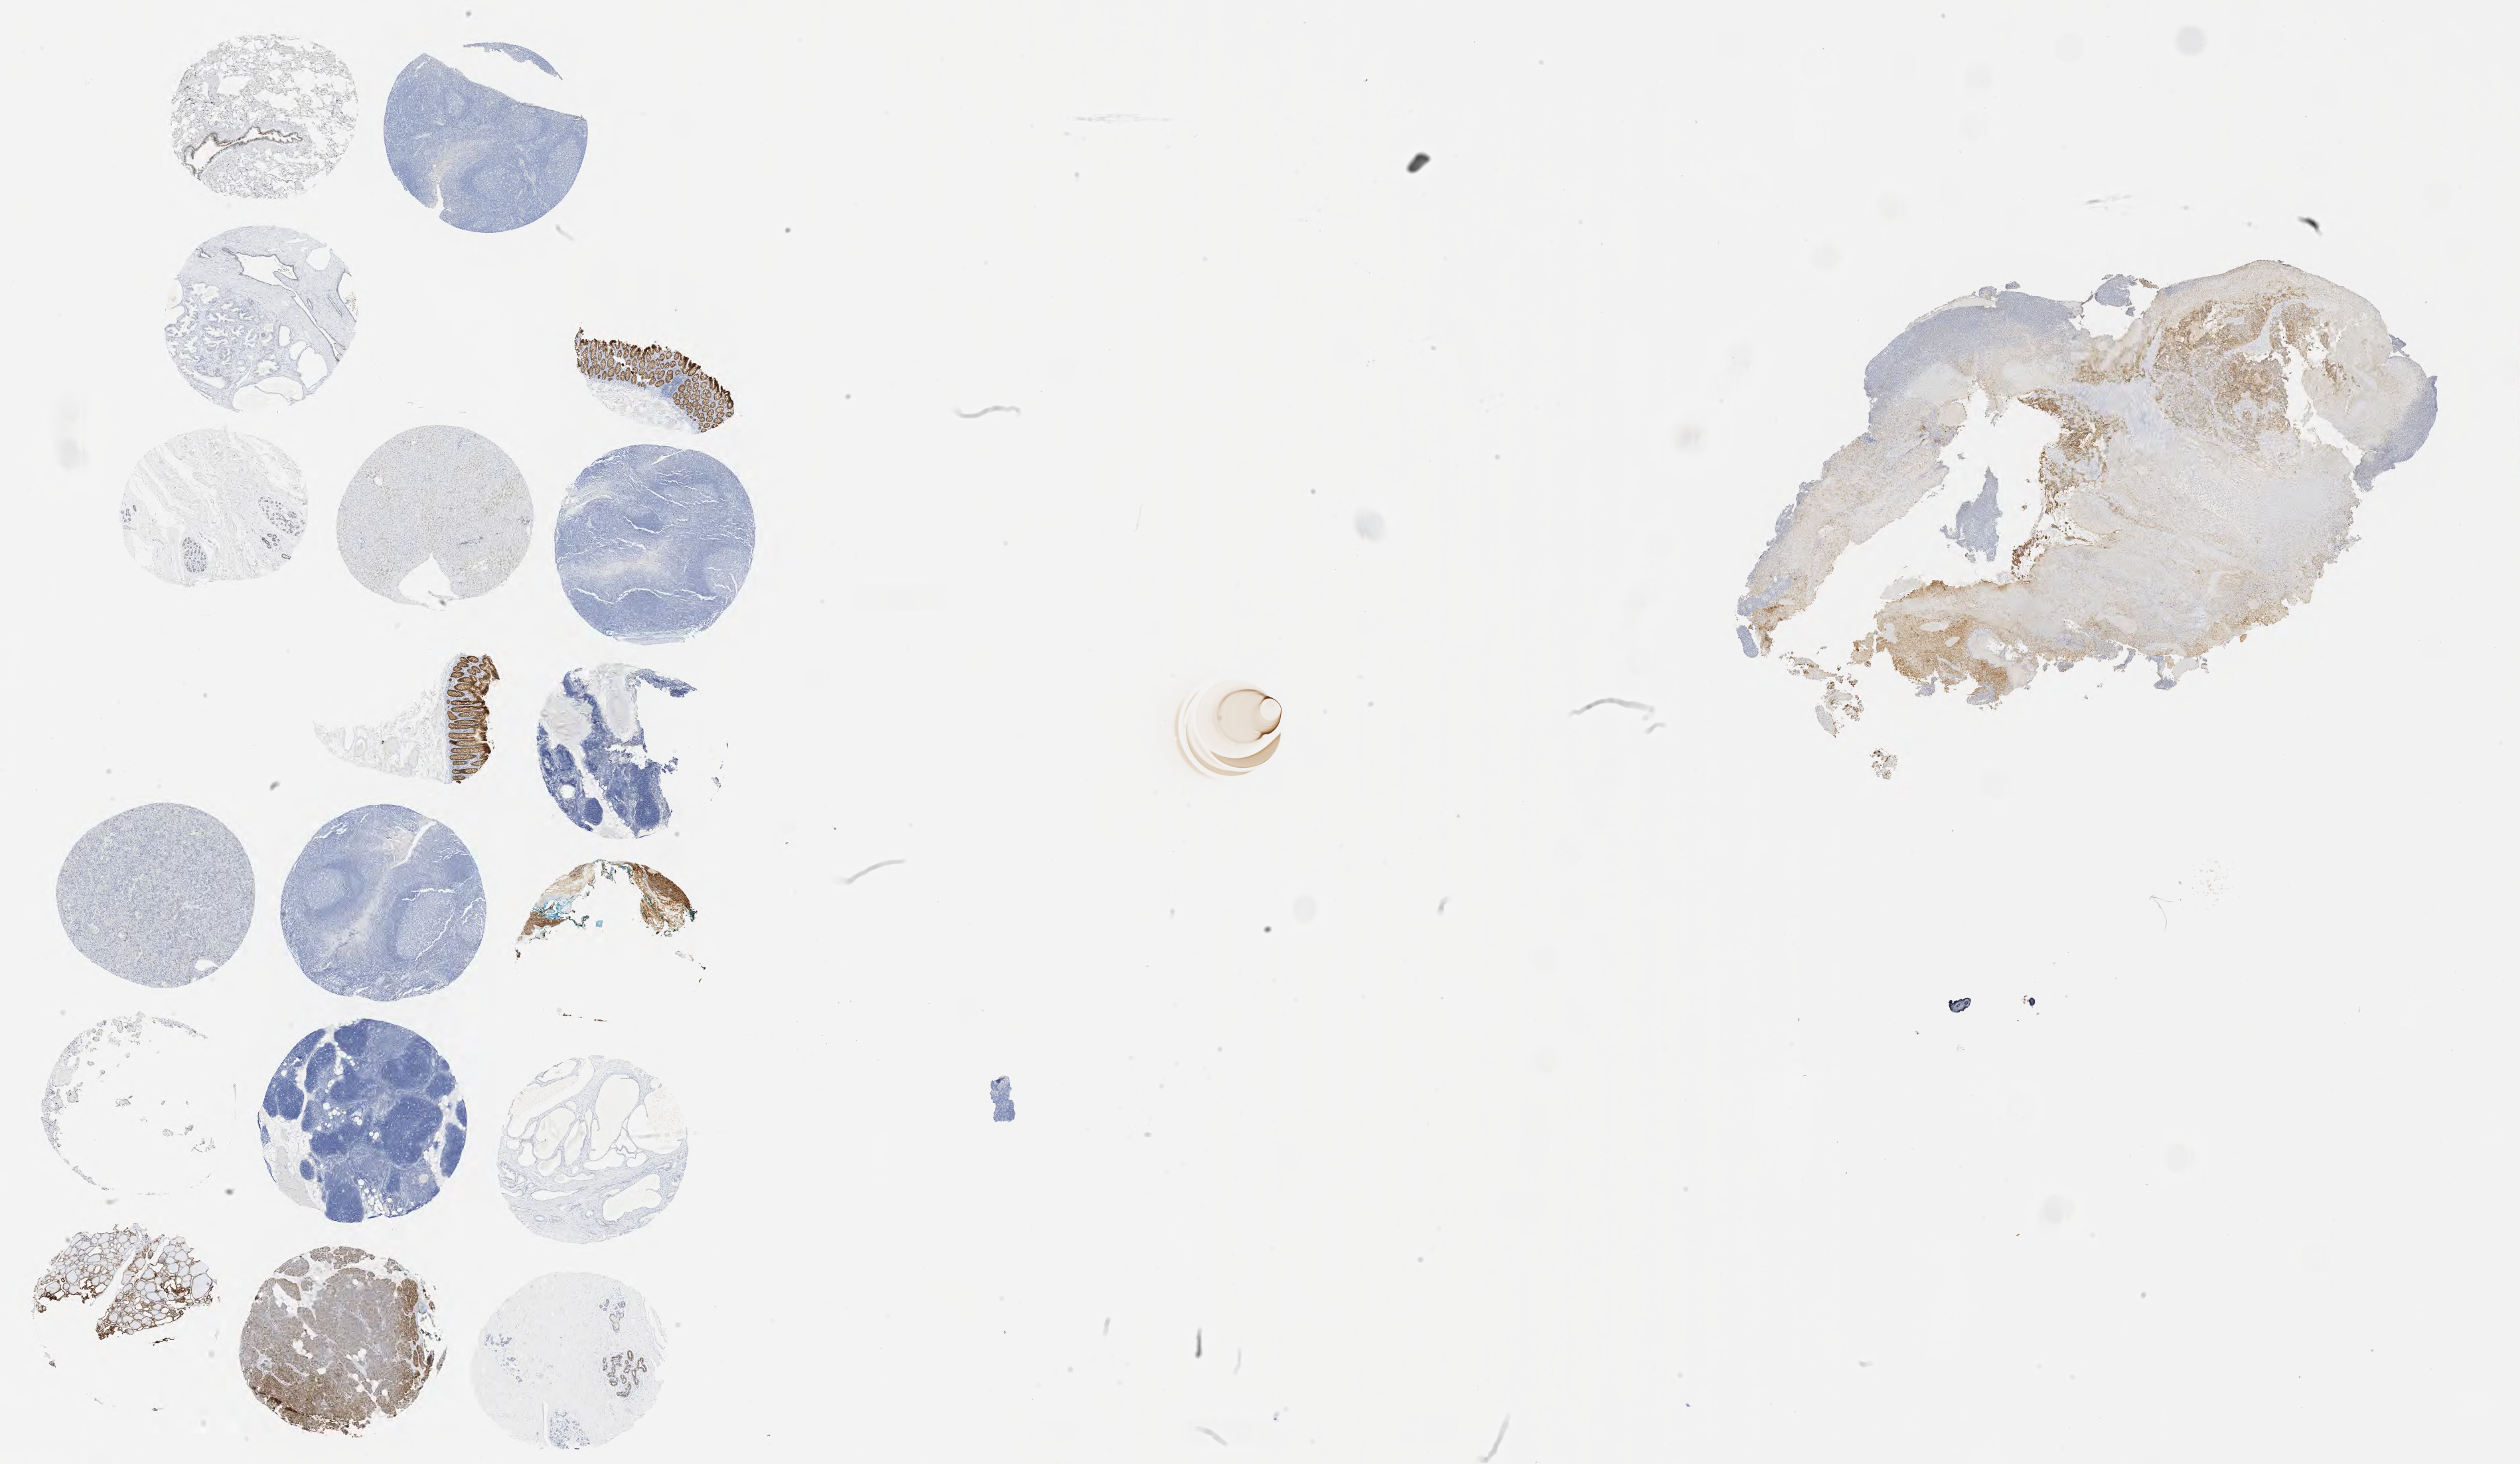
Immunohistochemistry (IHC) whole-slide image stained for Ber-EP4, a low-resolution overview of the entire scanned area, about 30.7 x 17.8 mm, specimen: tumor tissue, site: cervix. Patient female; age 62 years.
Diagnosis: Squamous cell carcinoma, large cell, nonkeratinizing, NOS.